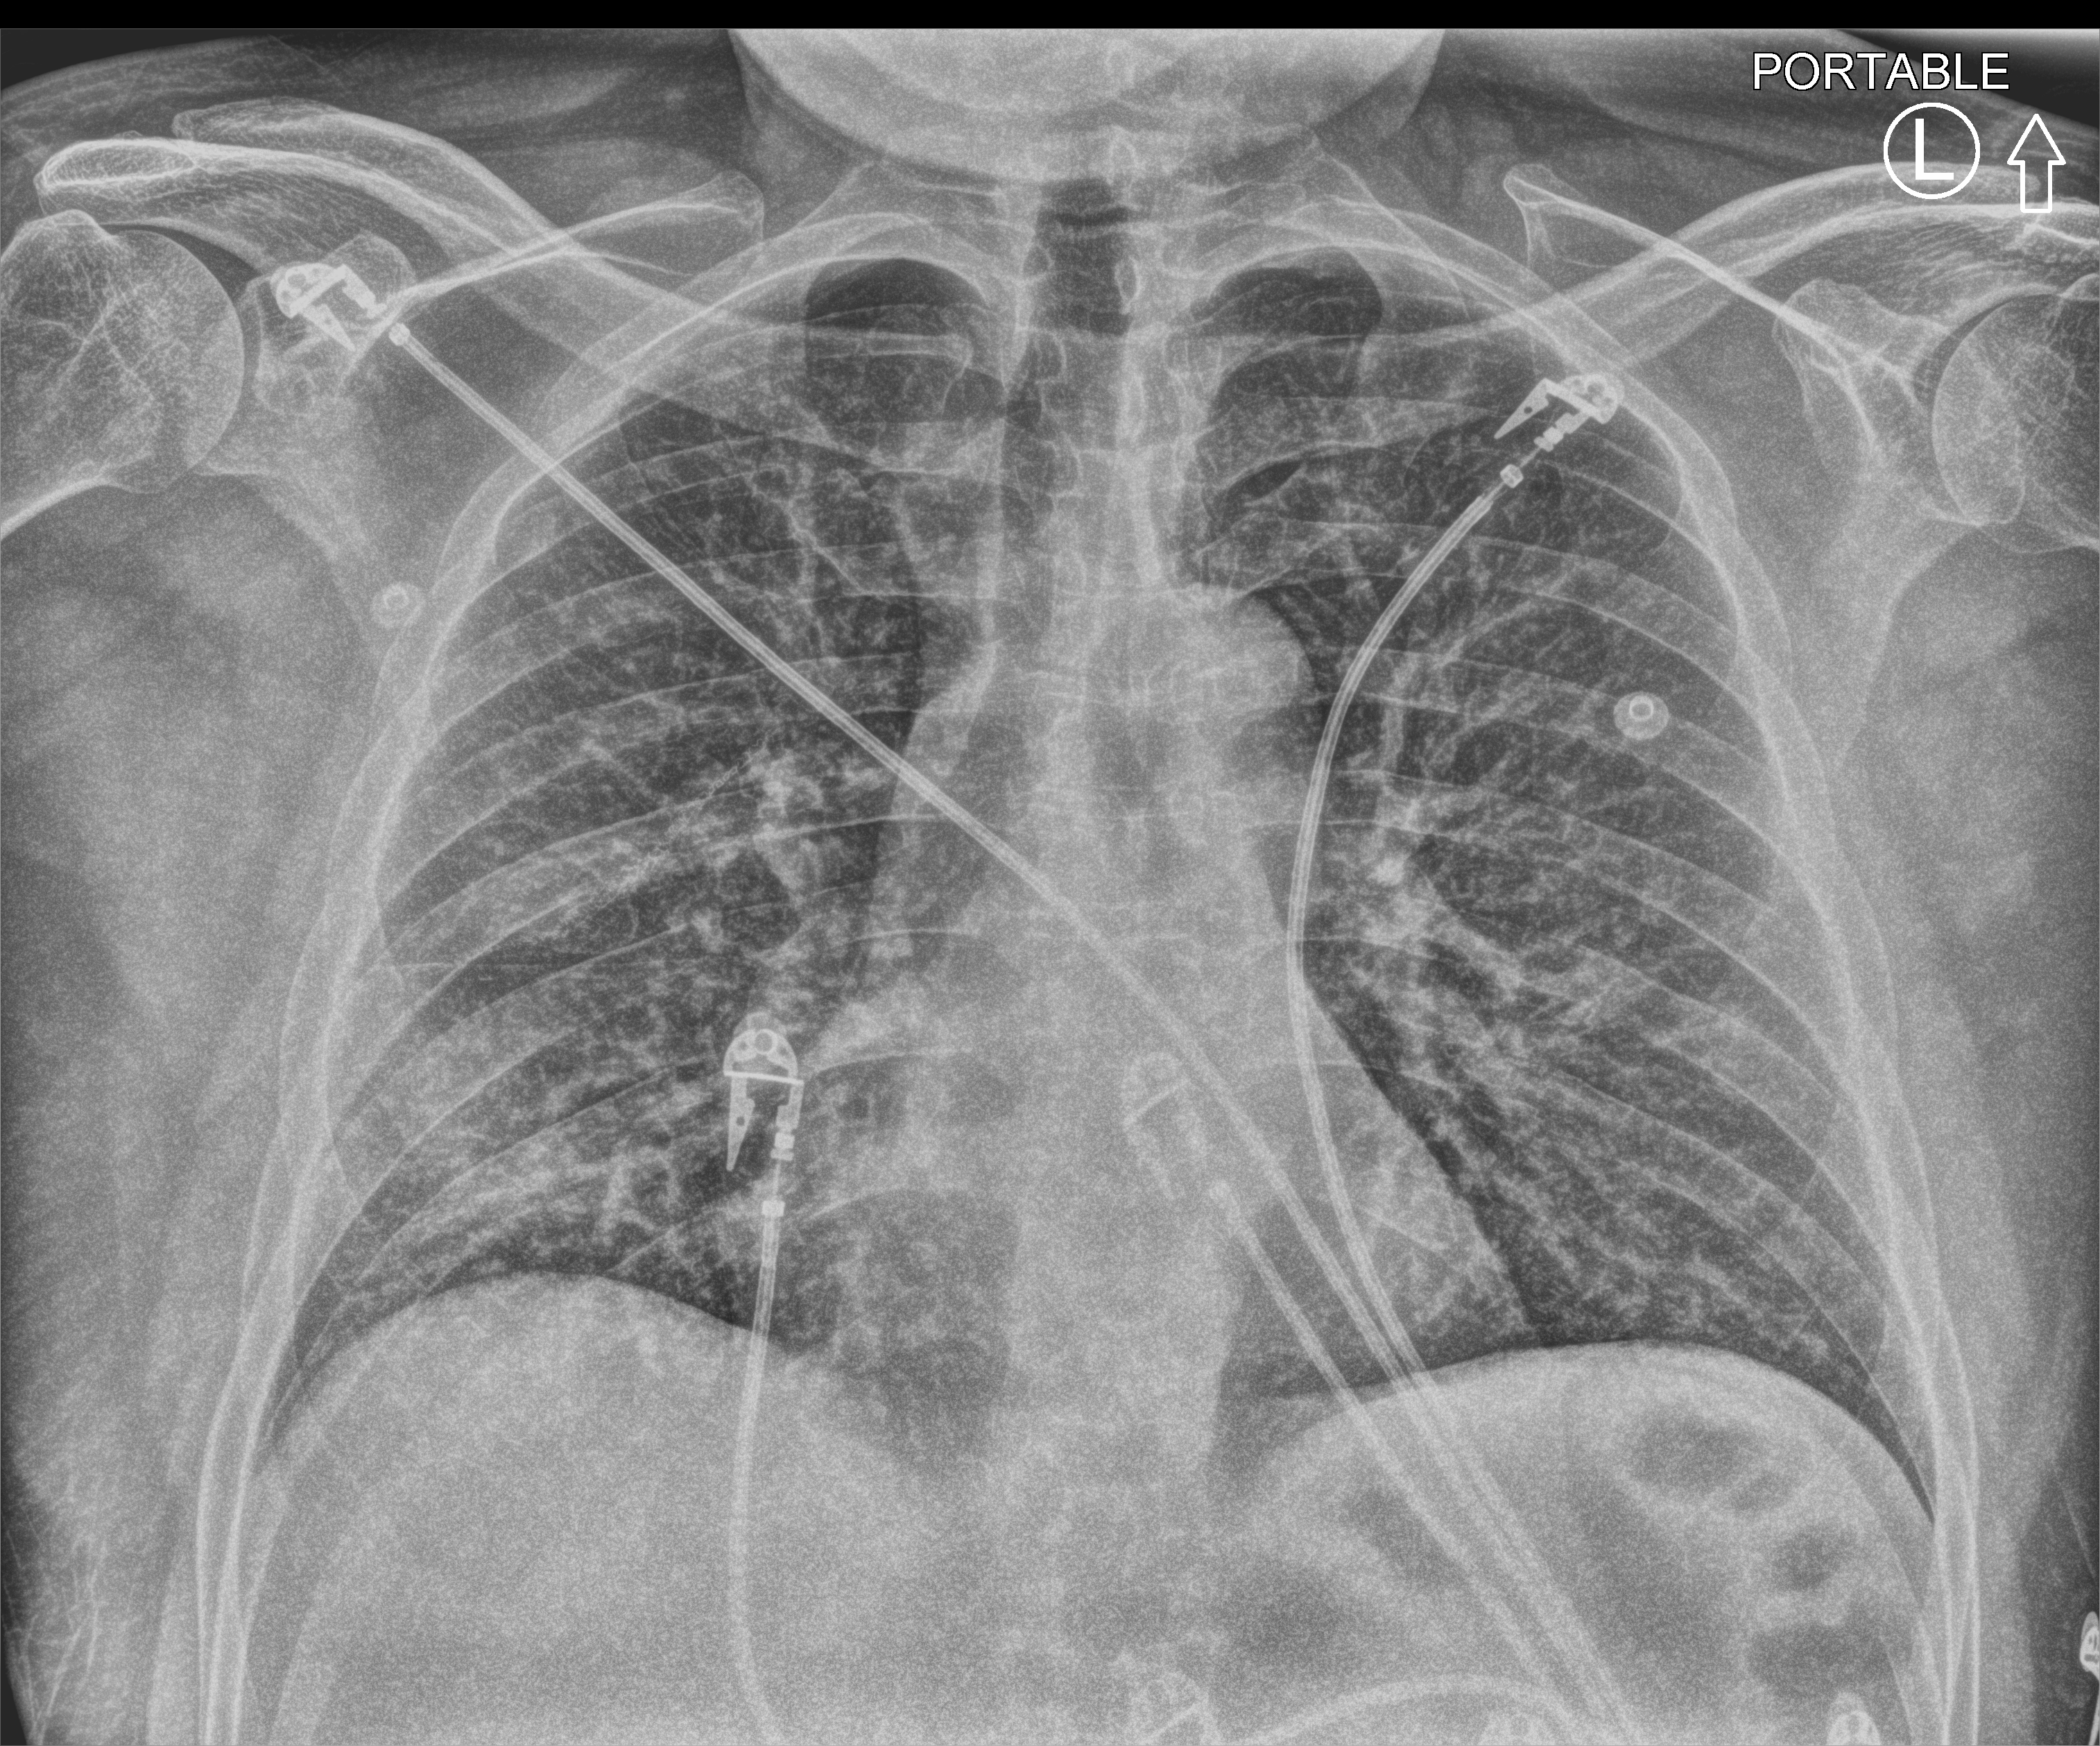
Chest X-ray (portable). Patient hospitalised with COVID-19; male, aged 18–59 years.
Admission-level facts for this patient (not findings on this image; timing relative to this image not recorded): length of hospital stay: 13 days.